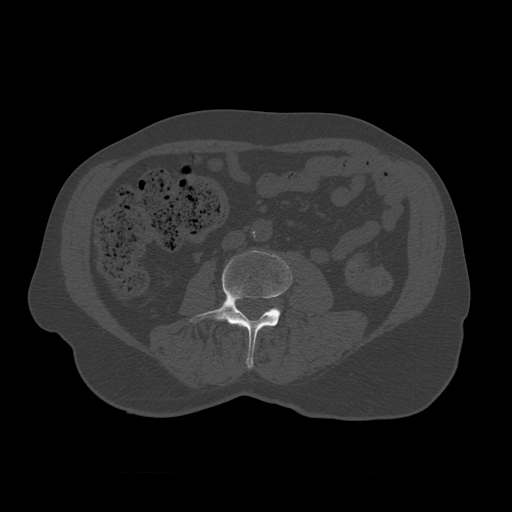
CT including the spine, one axial slice. Reconstruction kernel STANDARD. Bone window (W 1800 / L 400 HU). 1.25 mm slice thickness. 512 × 512 image matrix. Patient age 75 years. Case-level facts recorded for this patient, not image findings: primary cancer: prostate.
Structures marked on this image (semi-automatically segmented with operator editing):
- L3 vertebra: bounding box [x1, y1, x2, y2] px = [190, 250, 293, 369]